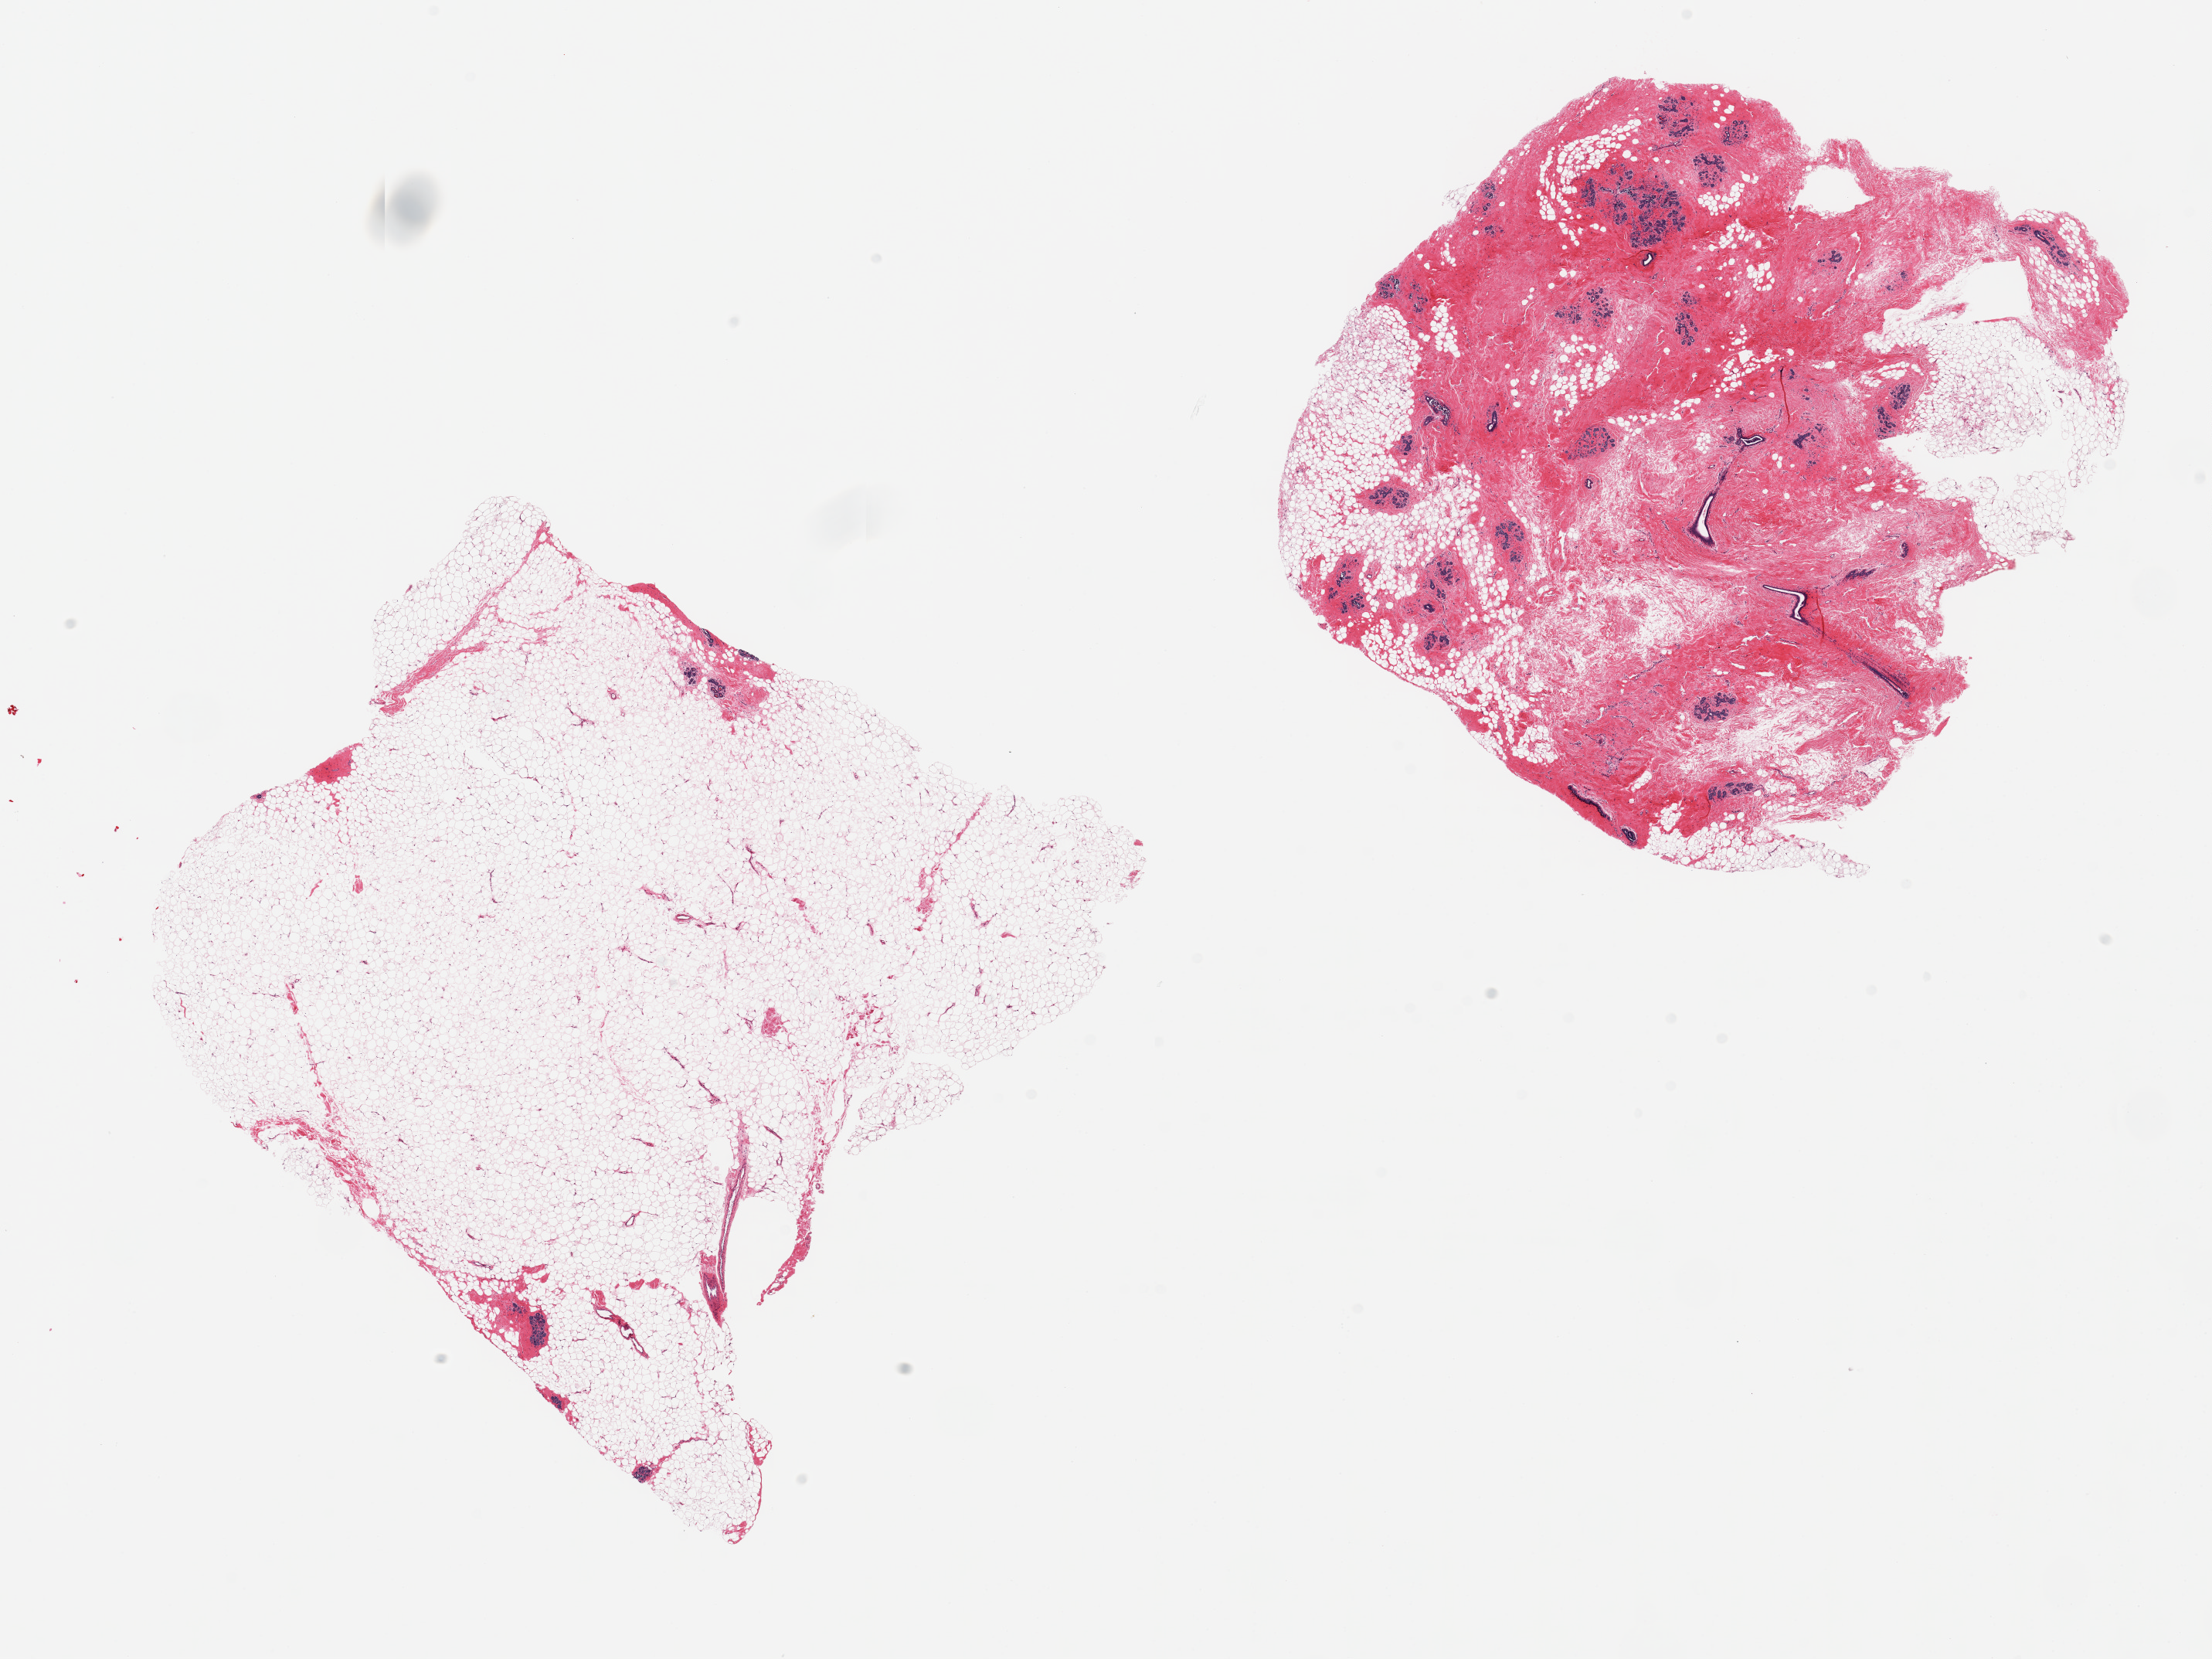
Digitized haematoxylin and eosin-stained section, low-resolution overview of the scanned area, about 22.6 x 17.0 mm; PAXgene-fixed, paraffin-embedded tissue; section of breast (target tissue); donor tissue sample. Donor: female.
Pathologist's review note for this sample: 2 pieces; 1 with ducts & lobules; 1 with >90% fat.